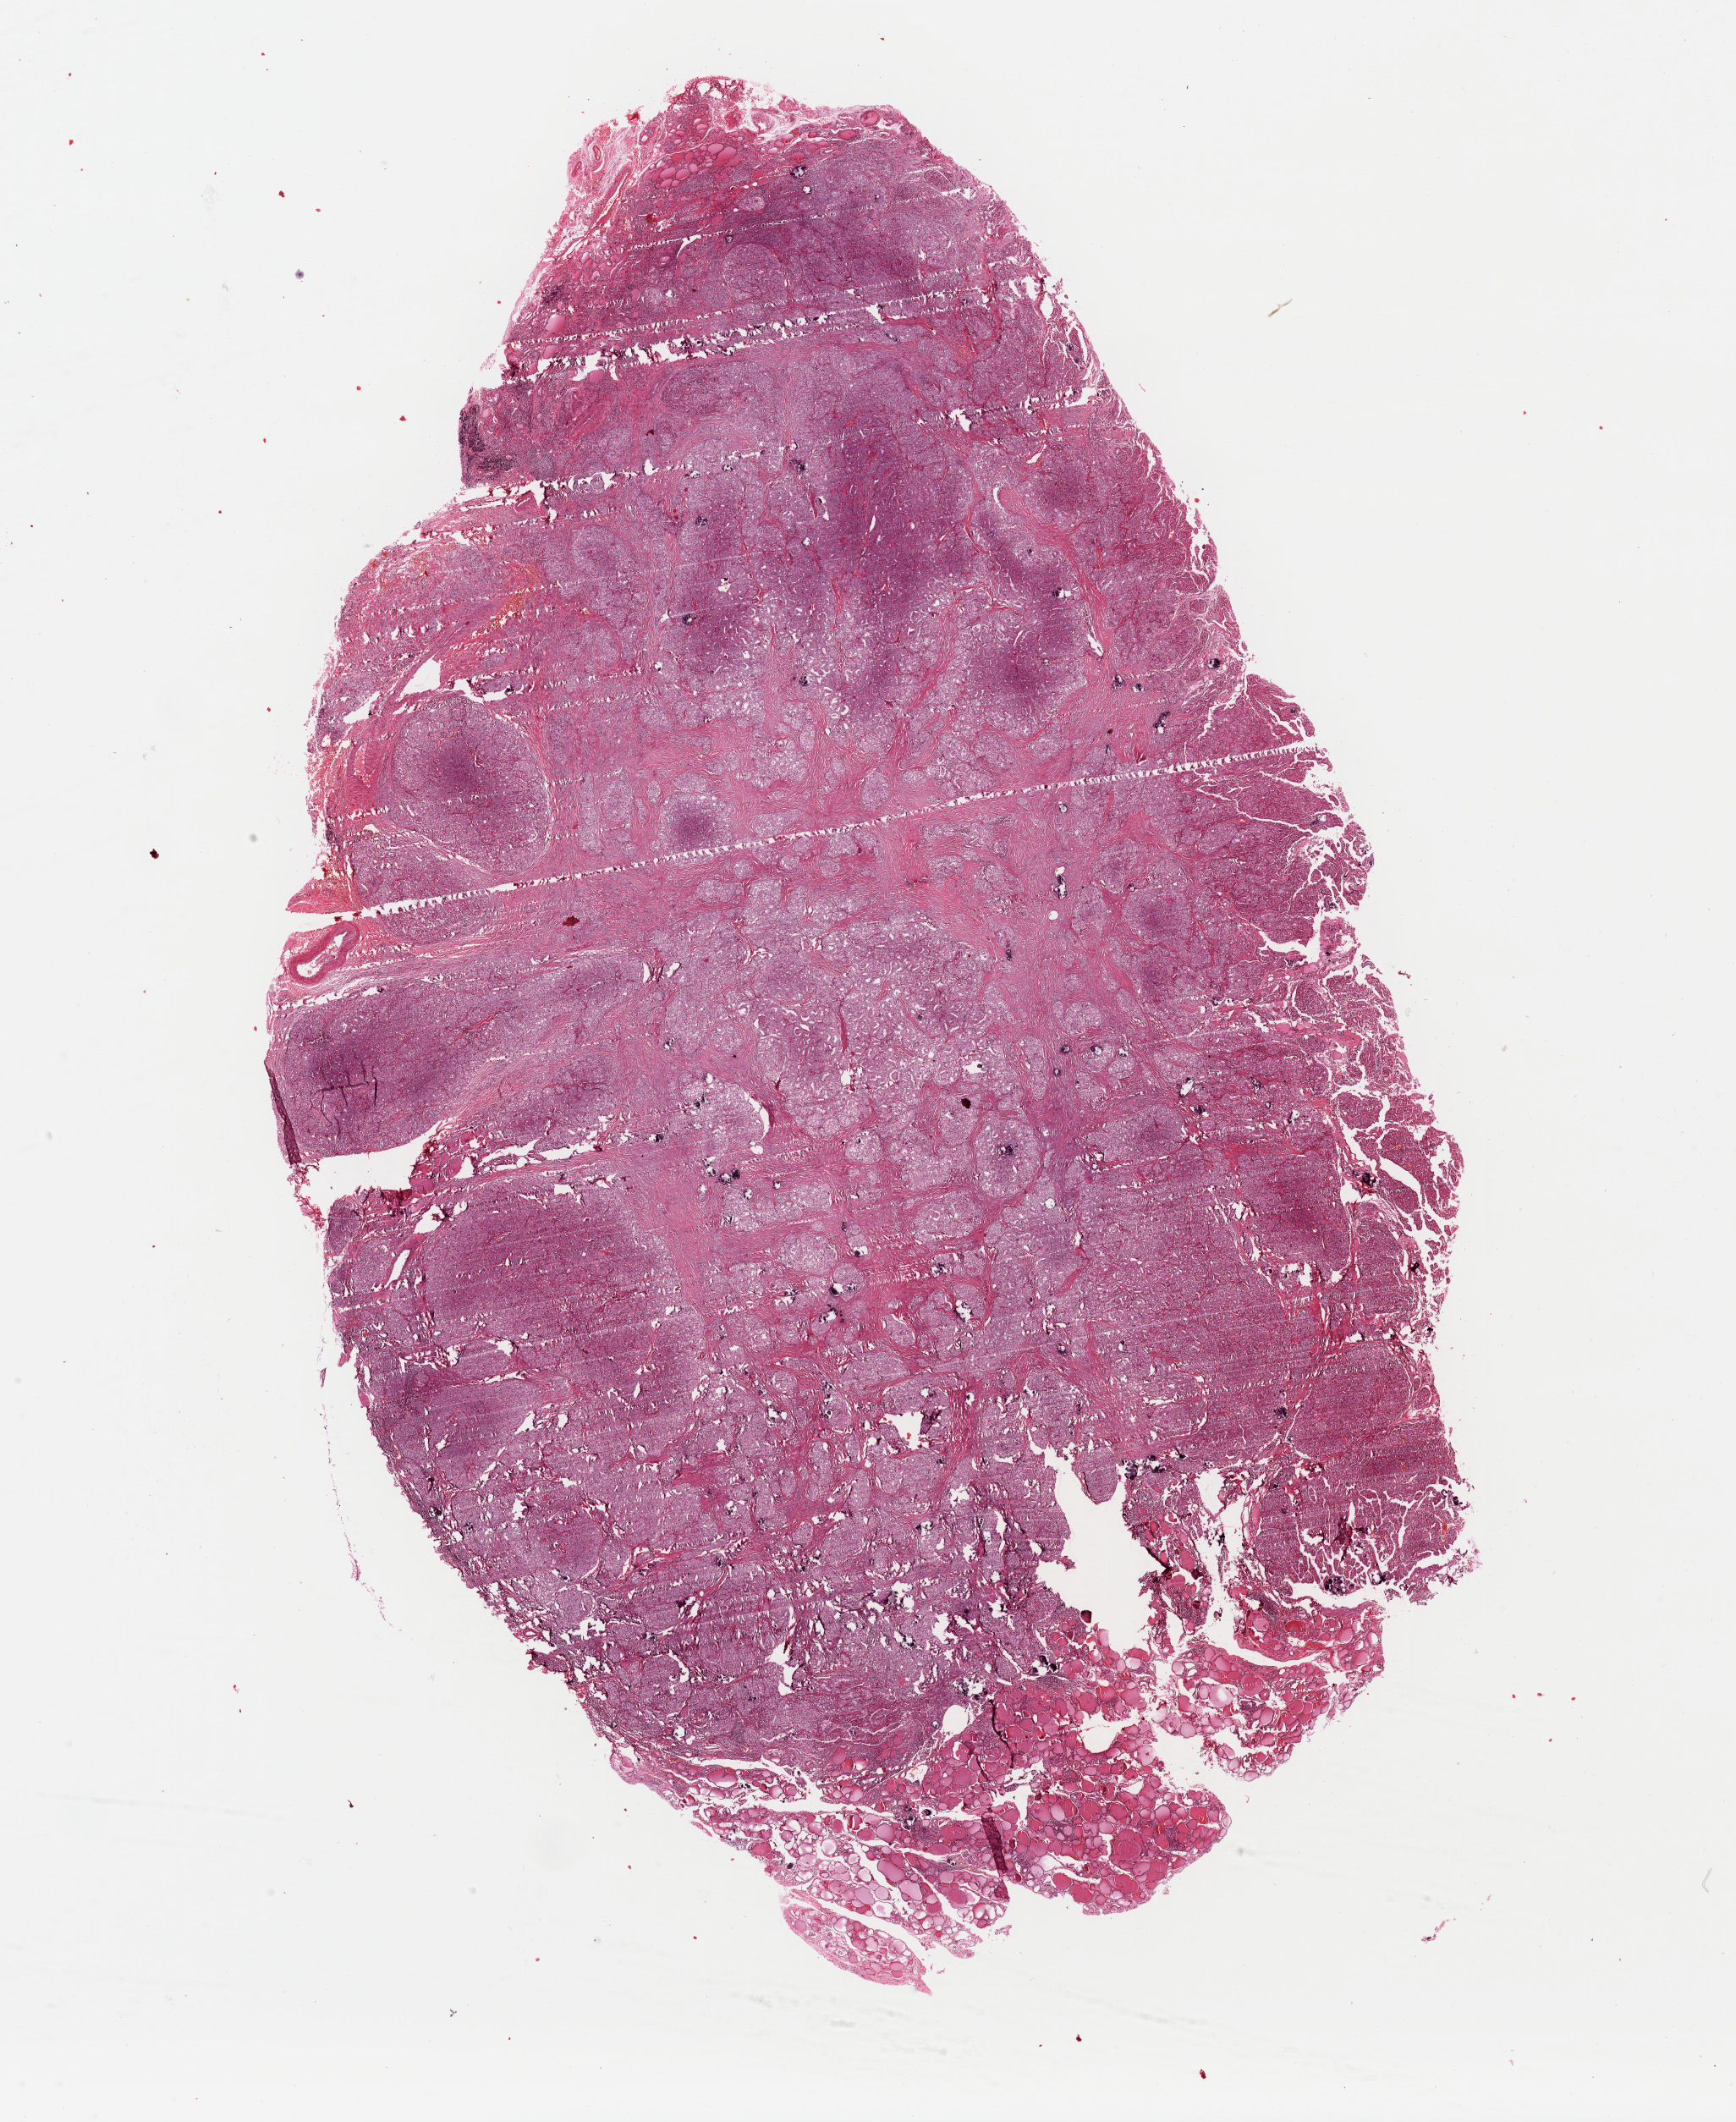
Whole-slide histology image, H&E-stained, shown as a low-resolution overview of the whole scanned area (about 16.2 x 19.8 mm), FFPE section, thyroid, primary tumour sample. Patient: female, age at initial diagnosis 41 years.
Histologic diagnosis: Papillary adenocarcinoma, NOS (thyroid gland). AJCC pathologic stage: I.